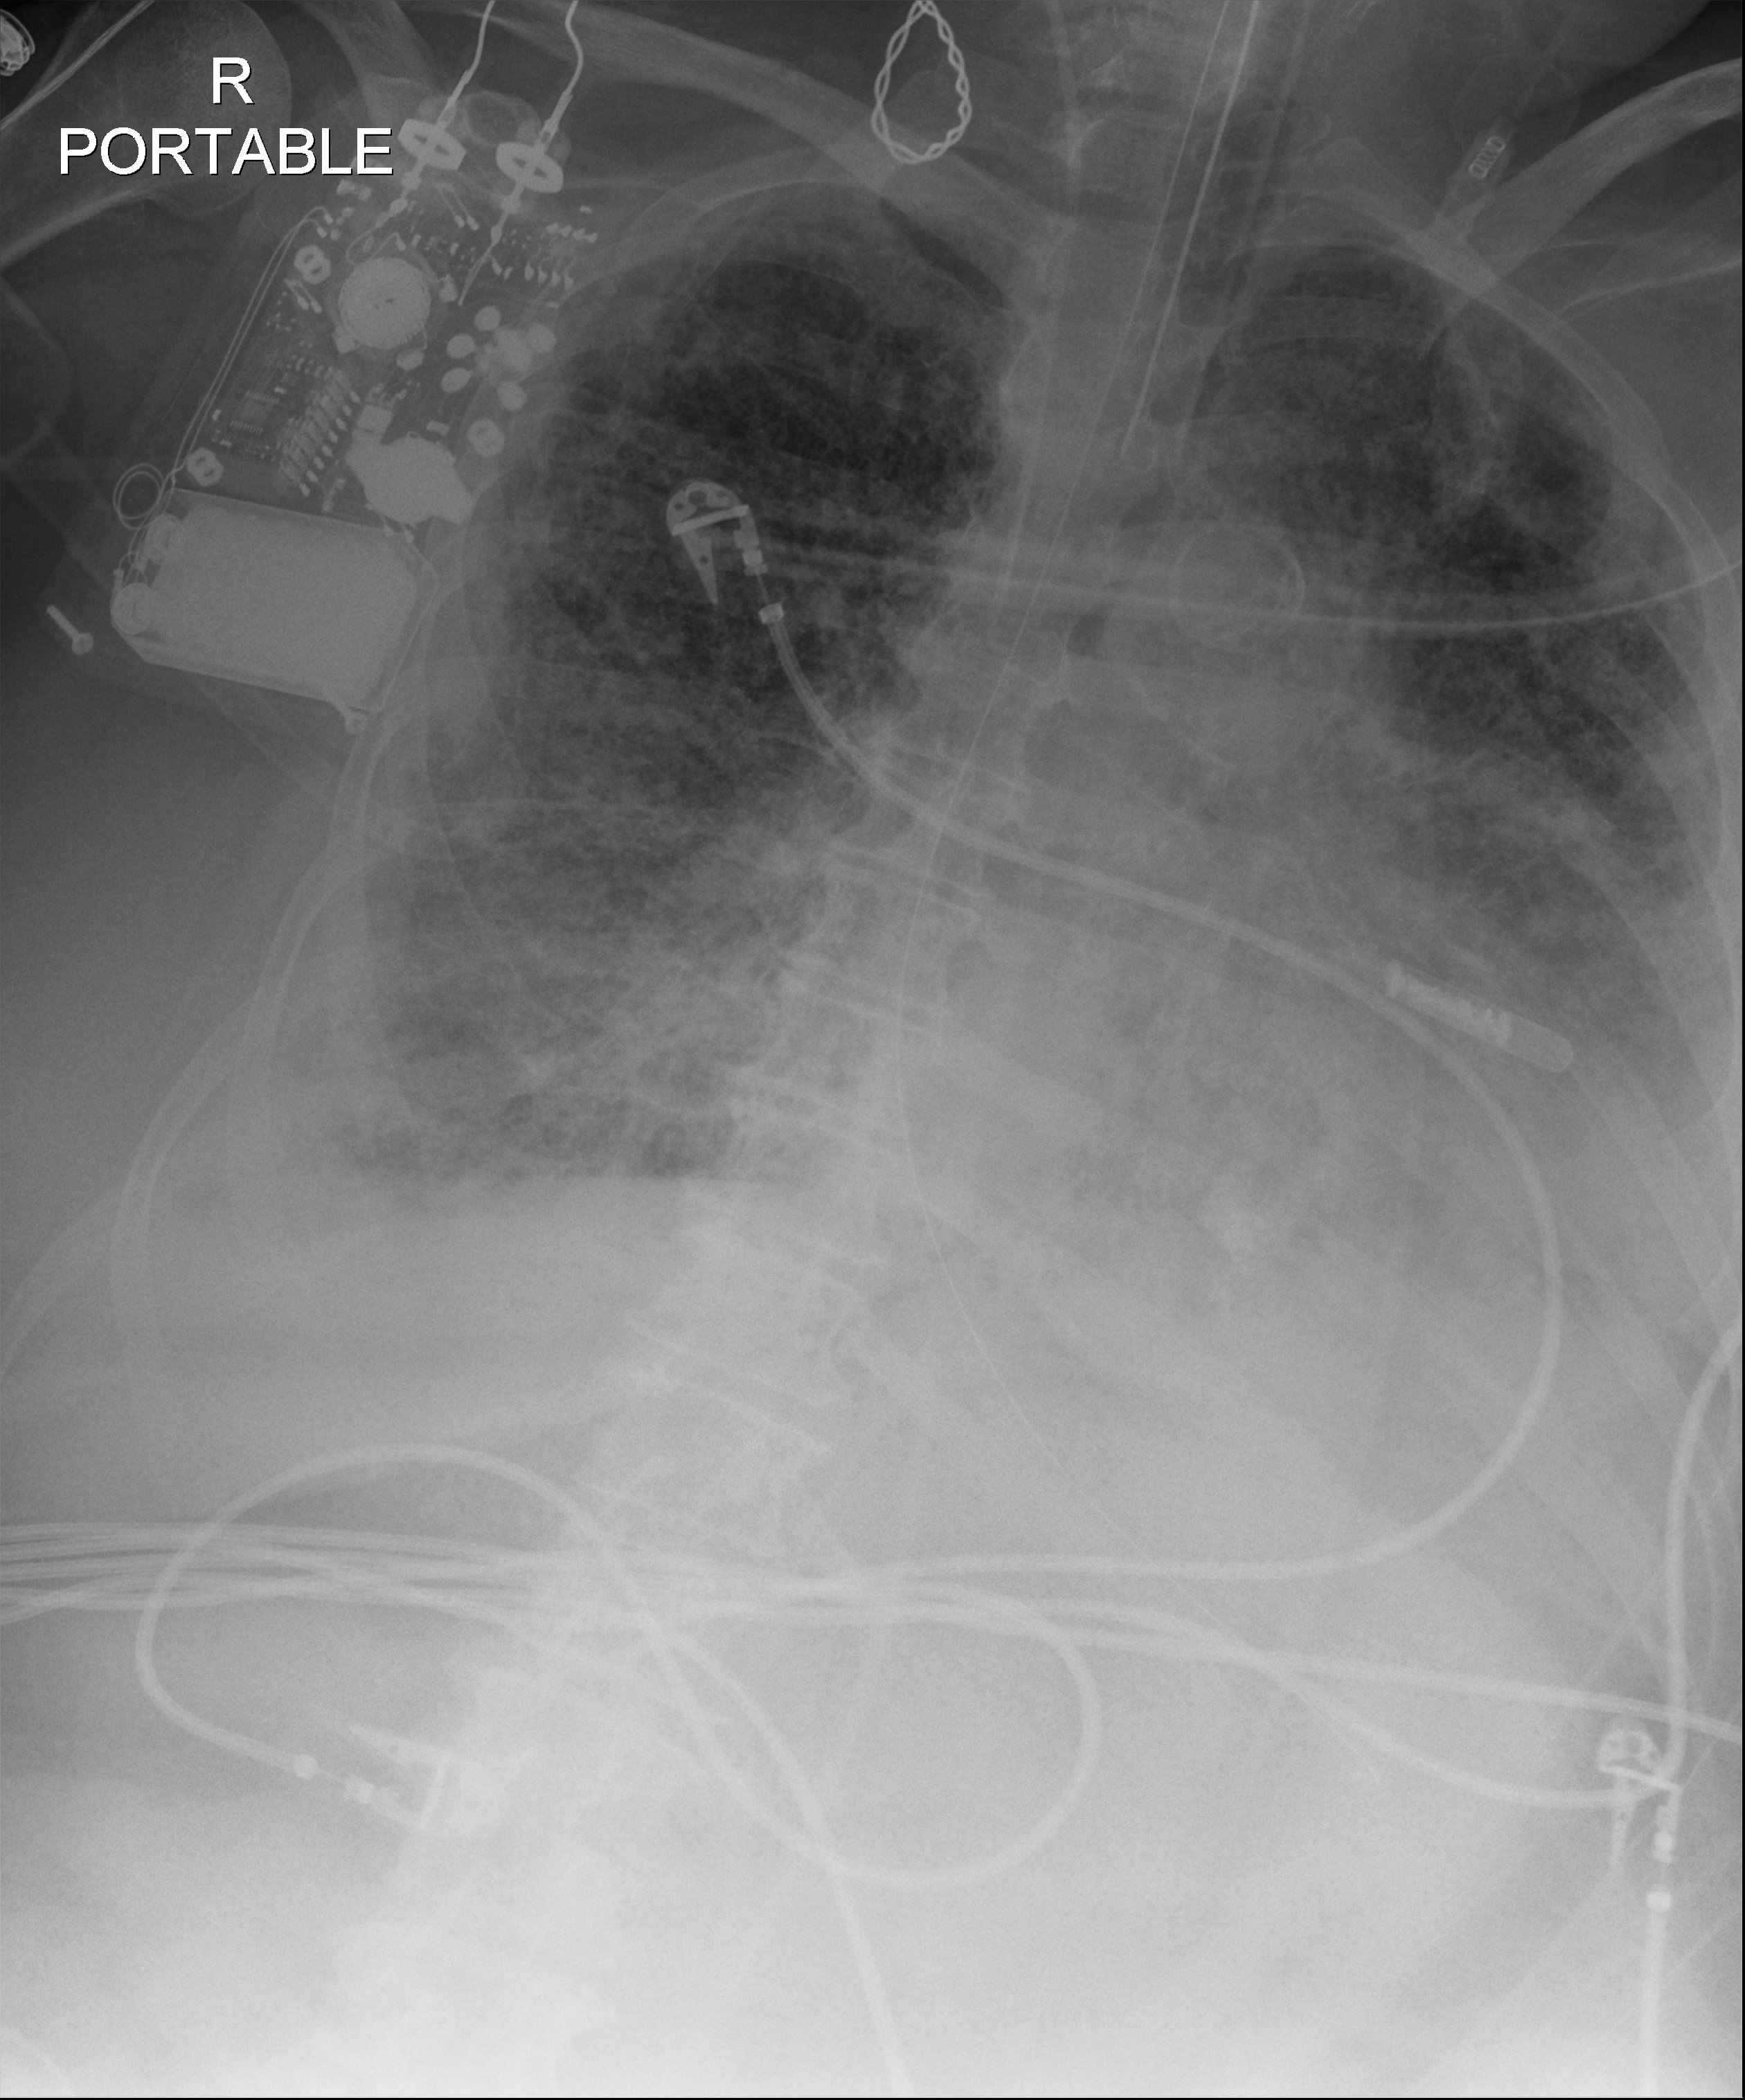
Portable chest radiograph. Female patient hospitalised with COVID-19, age 60–74 years.
Admission-level facts for this patient (not findings on this image; timing relative to this image not recorded):
- diabetes (admission record): yes